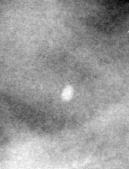
Crop from a digitized film mammogram around one marked abnormality, left breast, MLO view.
Calcifications, morphology lucent center / punctate; BI-RADS assessment category 2; subtlety rating 5 on a 1 (subtle) to 5 (obvious) scale; benign without callback (not worked up further).